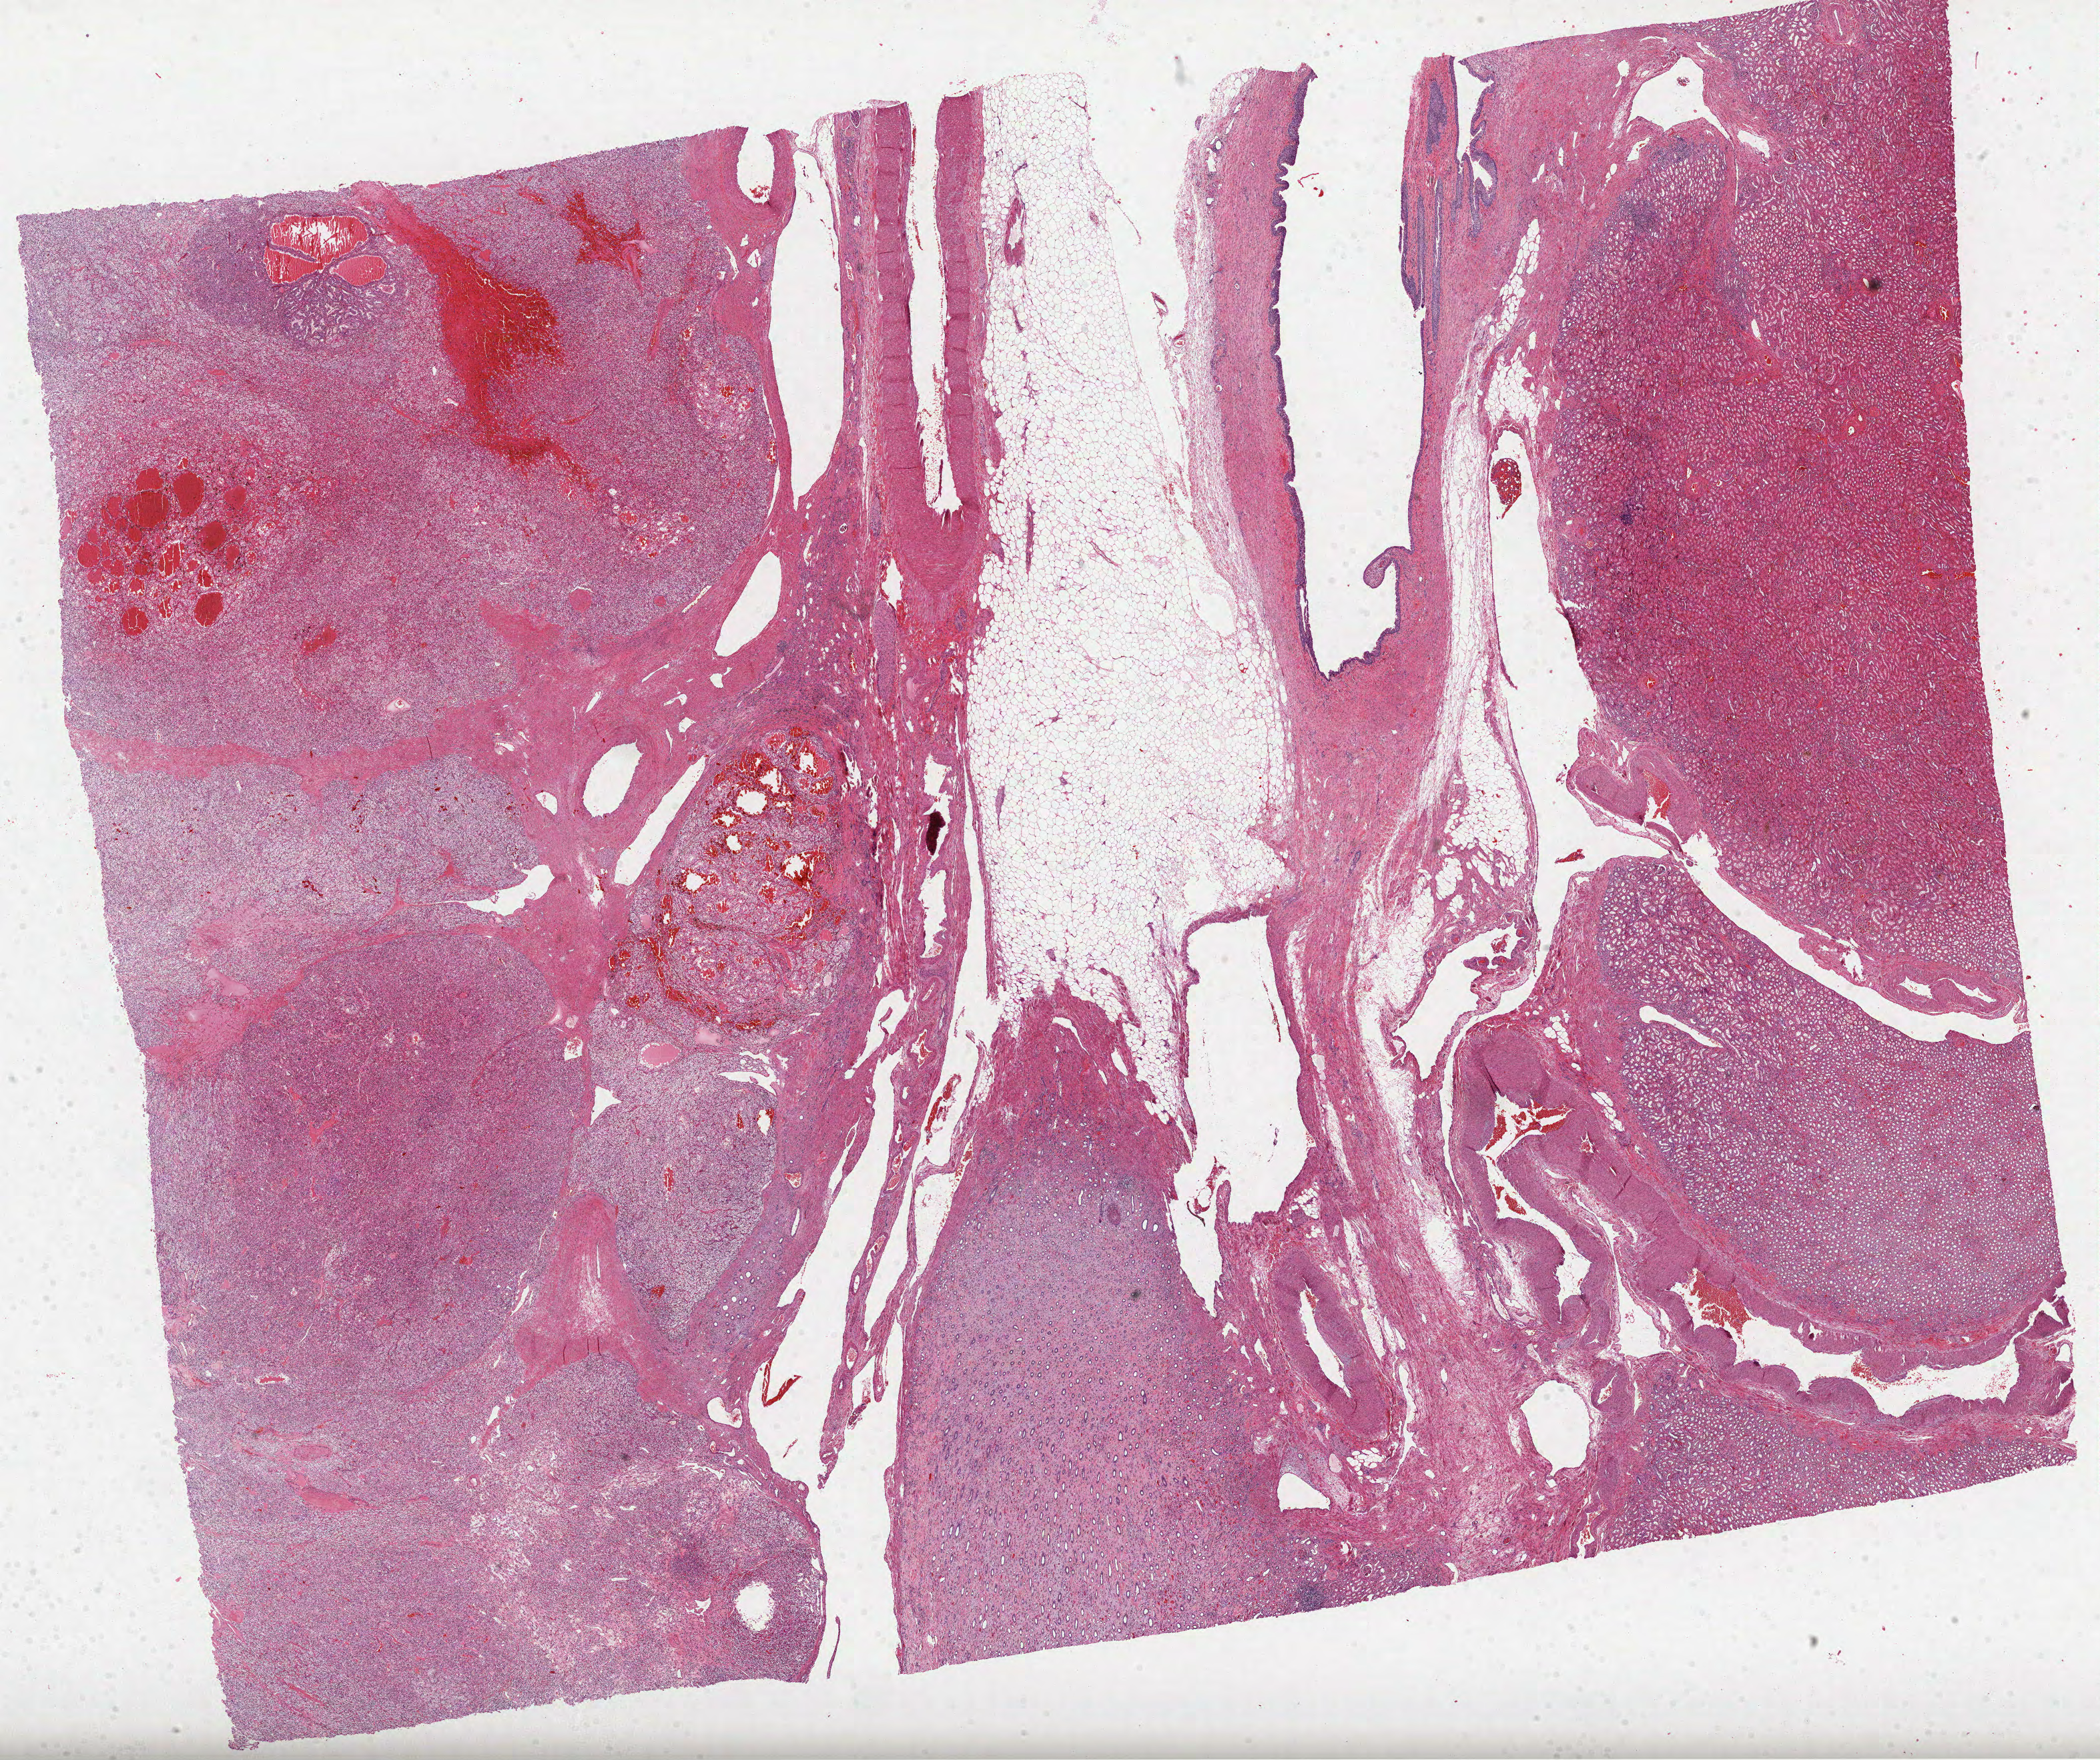
Digitized H&E tissue section (whole slide), shown as a low-resolution overview of the whole scanned area (about 25.4 x 21.3 mm), FFPE section, primary tumour sample from the kidney. Male patient; age at initial diagnosis 69 years.
Pathologic diagnosis: Clear cell adenocarcinoma, NOS.